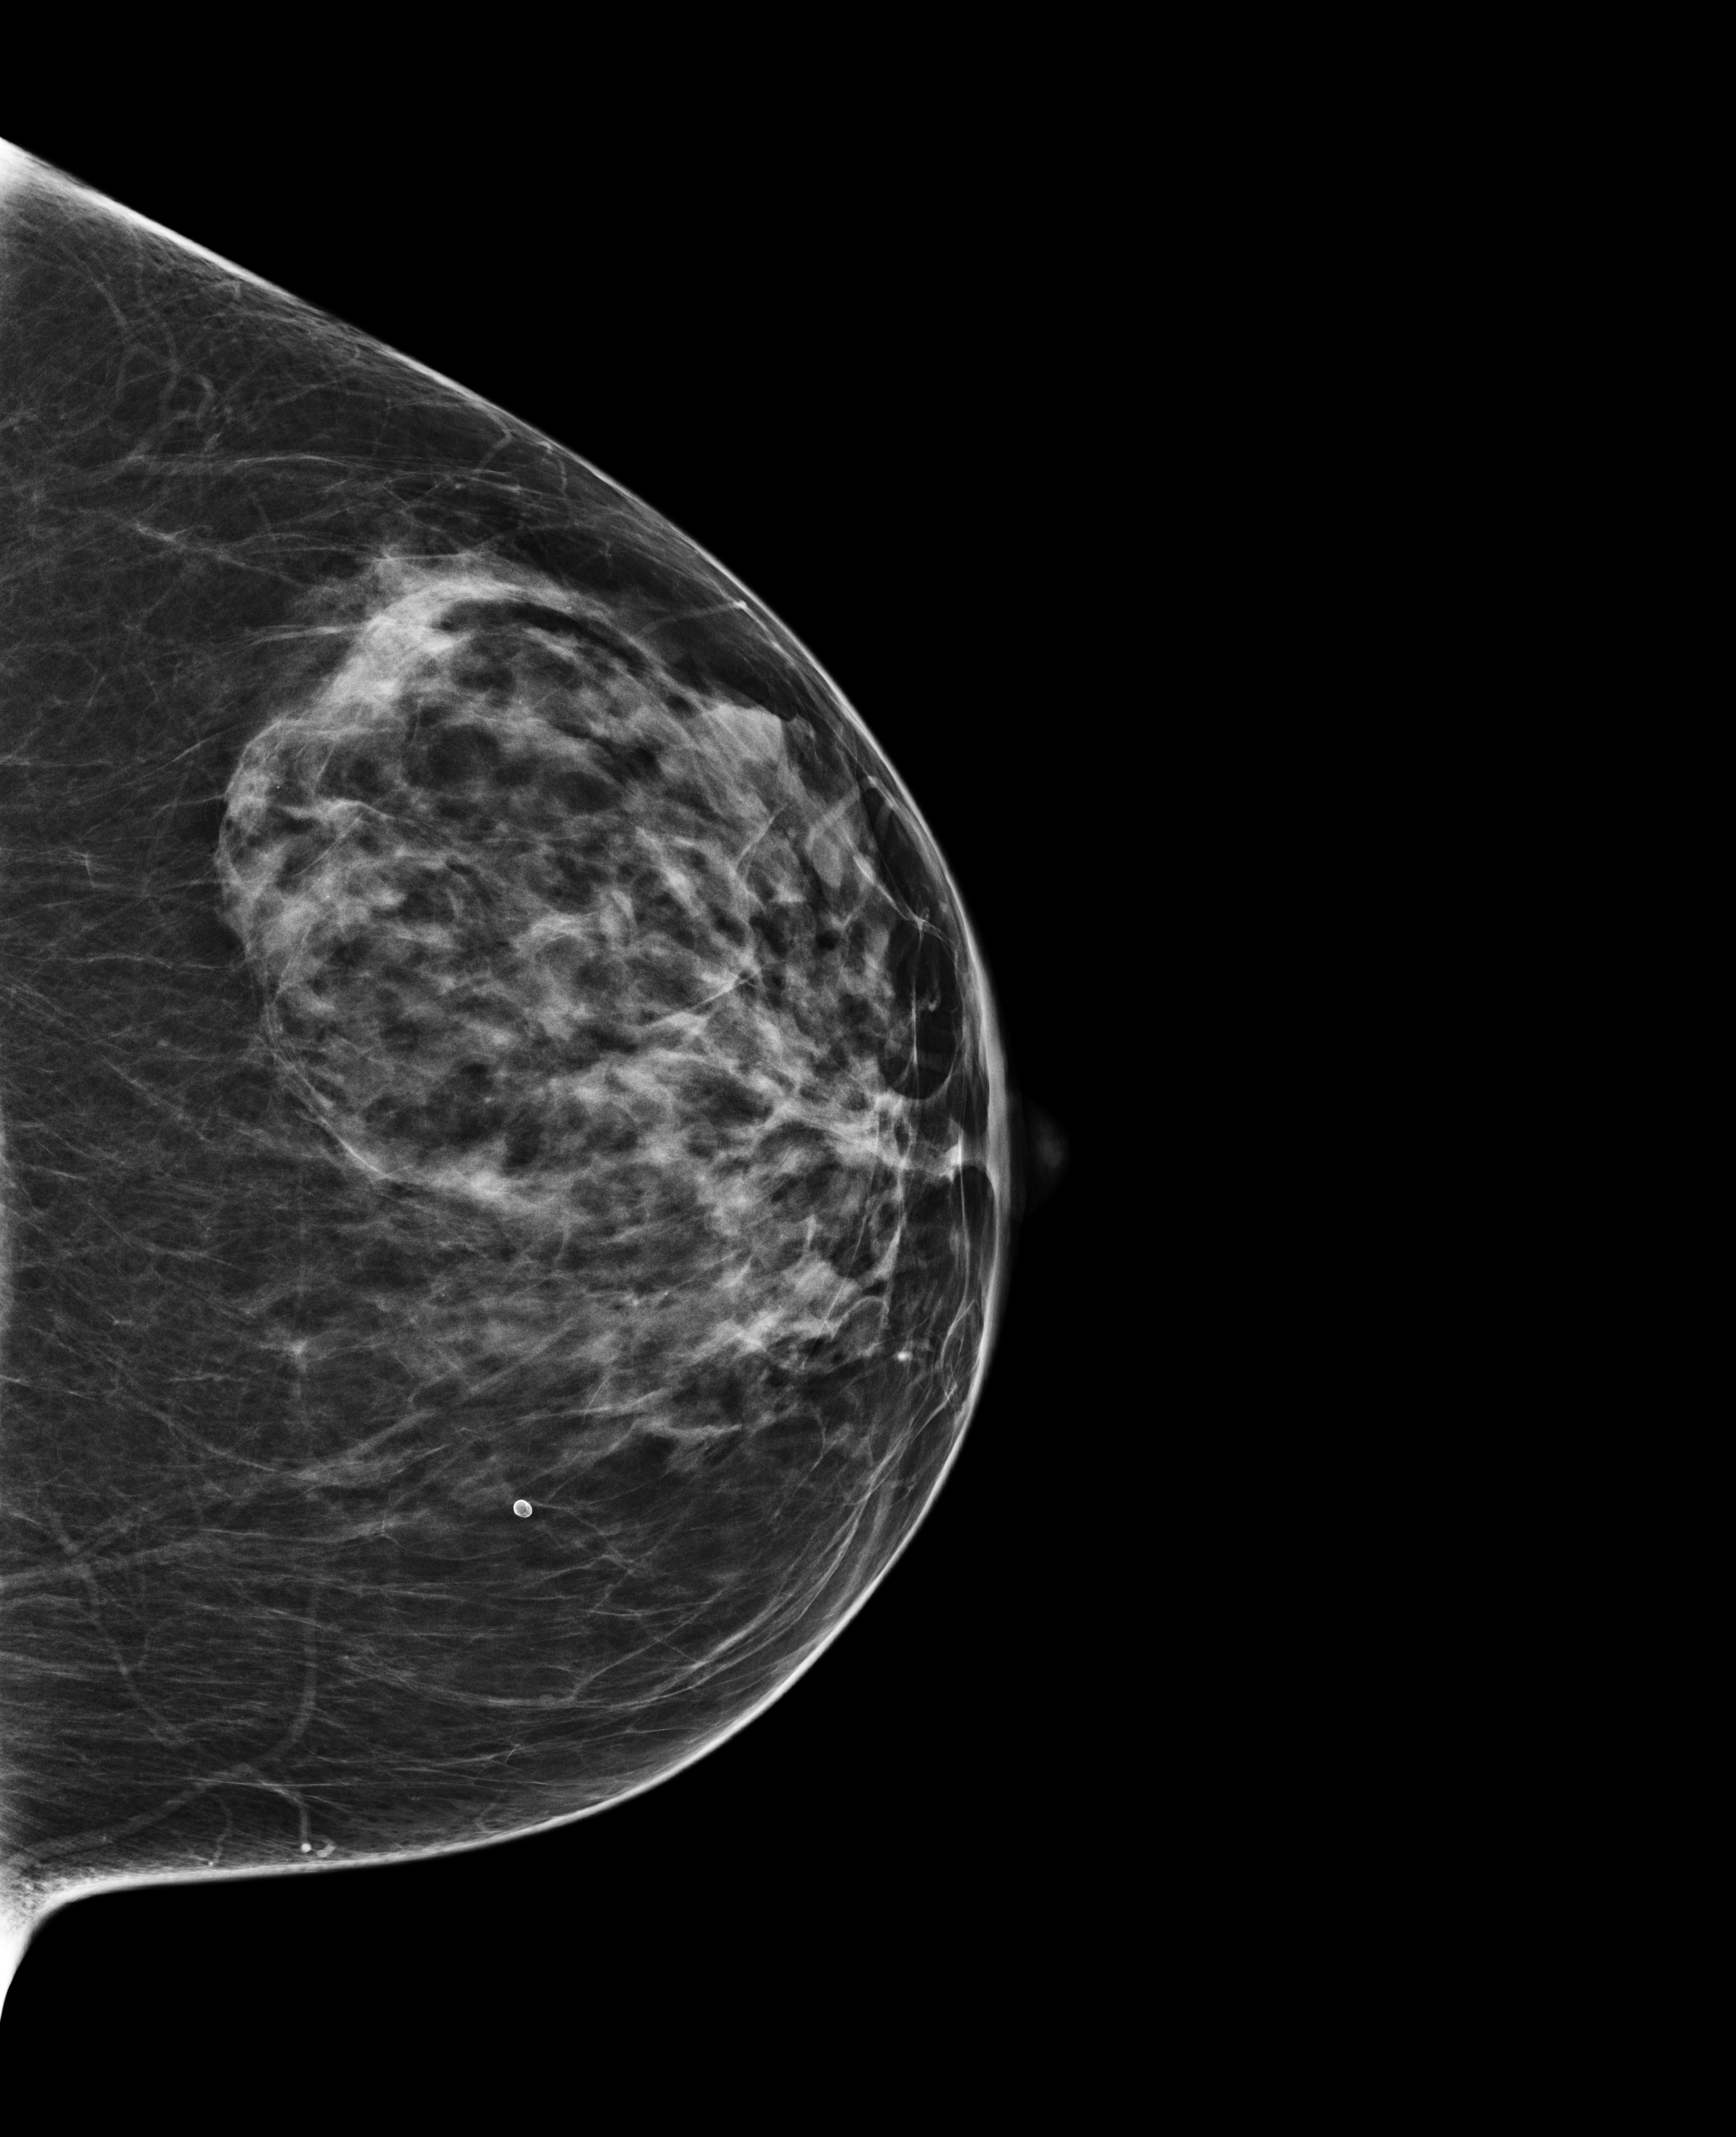
Annual screening mammography examination; system: Selenia Dimensions. Patient: female, 58 years.
Image type: full-field digital mammogram. Breast: left. Projection: CC view.